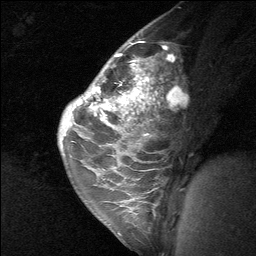
Breast MRI (dynamic contrast-enhanced), one sagittal slice. Dynamic contrast-enhanced study with each time point stored as its own series, time point 2 of 3 at this slice position (early post-contrast, ordered by acquisition time). 1.5 T. TE 4.8 ms, TR 27 ms. 256 × 256 image matrix, field of view 180 × 180 mm. Female patient, age 26 years. From the clinical record (not read from this slice): setting: breast cancer imaged before/during neoadjuvant chemotherapy; receptor status: HR-positive, HER2-negative.
Annotated regions visible in this slice (semi-automatic segmentation, software-assisted and operator-edited):
- analysis volume of interest (the breast-tissue region the enhancement analysis was run in; not a lesion): bounding box (x1, y1, x2, y2) in pixels: (86, 43, 169, 138)
- tumour enhancement mask (voxels above the 90 % enhancement threshold inside the analysis volume of interest): (91, 54, 151, 116)